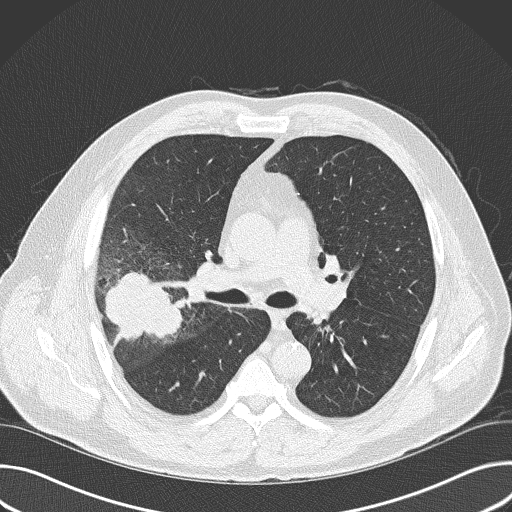
Axial slice from a low-dose chest CT screening exam, baseline annual screen, lung window (W 1500 / L -600 HU), 2 mm slice thickness, slice 99 of 157 in the series, 512 × 512 image matrix, field of view 380 × 380 mm. Male, age 56 years at enrolment. Current smoker at enrolment.
Expert reader's lesion annotation, bounding box (x1, y1, x2, y2) in pixels: (81, 259, 185, 364). Reader record for this screening exam (exam-level; its link to the box is not recorded): non-calcified nodule or mass ≥4 mm, right upper lobe, 6 × 5 mm, spiculated (stellate) margins, soft tissue attenuation. Participant outcome: lung cancer diagnosed 16 days after this screen — adenocarcinoma, NOS, right upper lobe, poorly differentiated (G3), stage IIB (AJCC 6th edition), 60 mm at pathology.